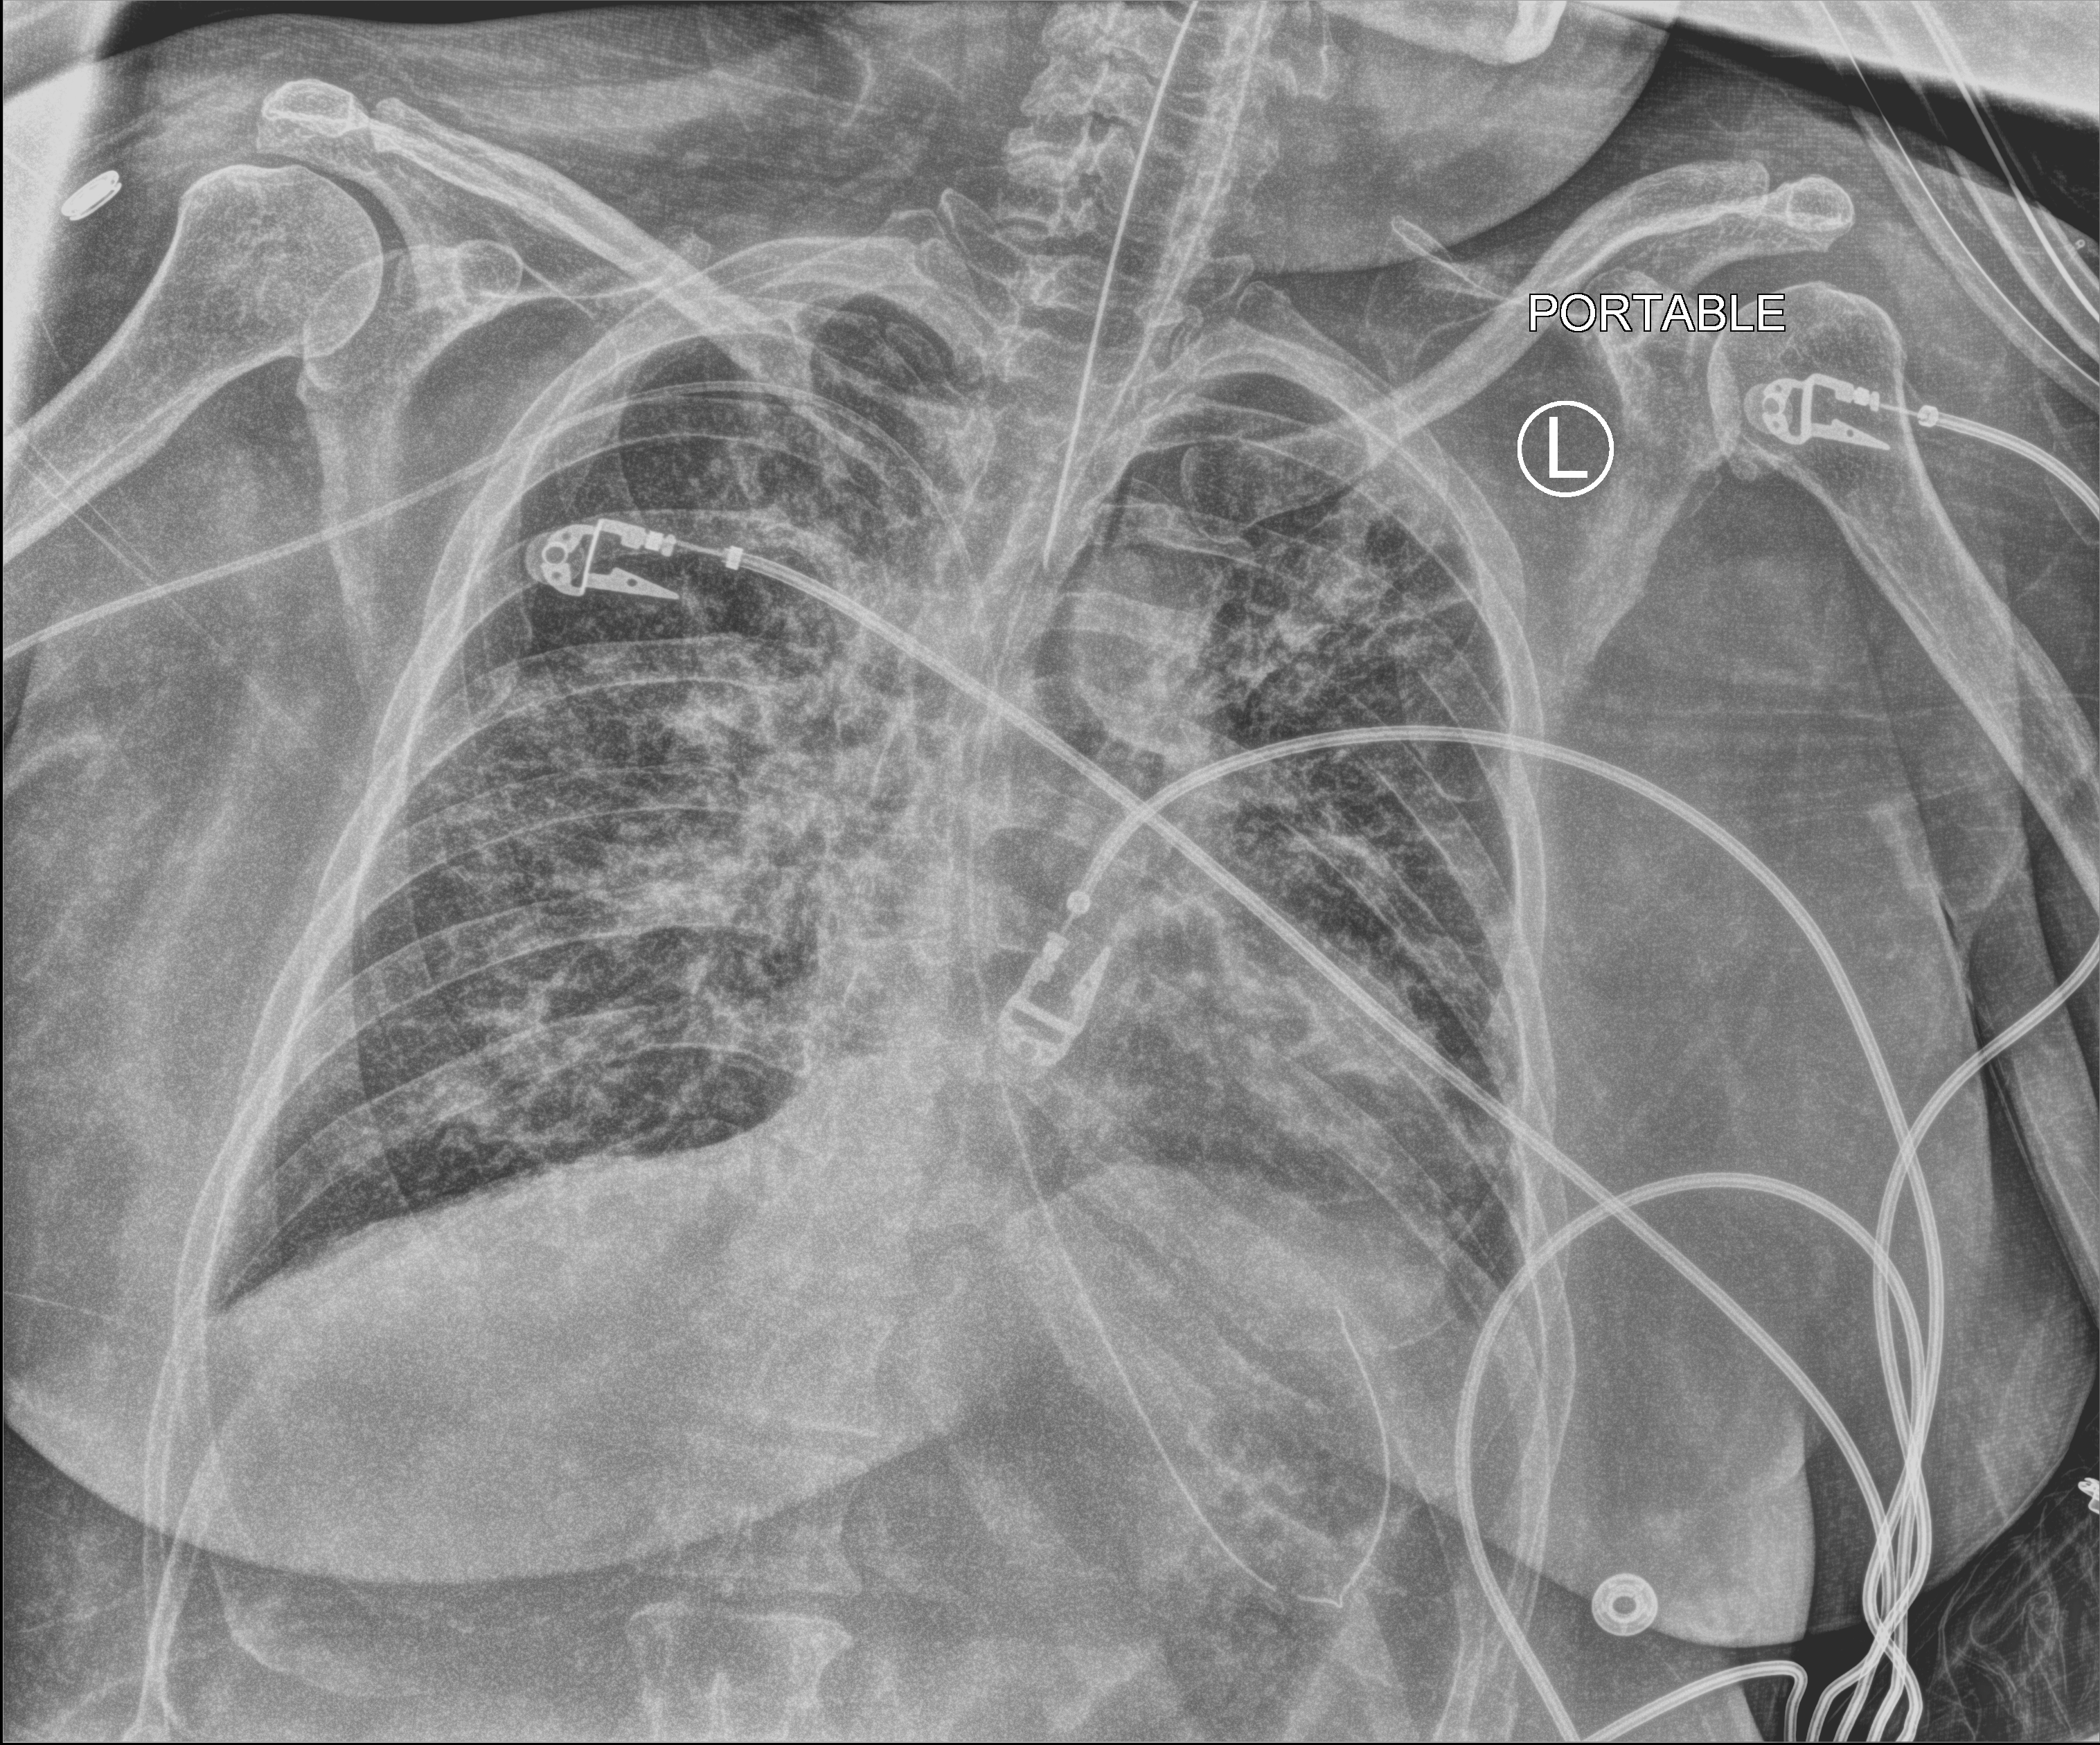
Portable chest radiograph; anteroposterior (AP) projection. Adult patient hospitalised with COVID-19, age 18–59 years.
Hospital-stay facts (about this admission, not read from this image; timing relative to this image not recorded): admitted to intensive care during this hospital stay: yes; mechanically ventilated during this hospital stay: yes.